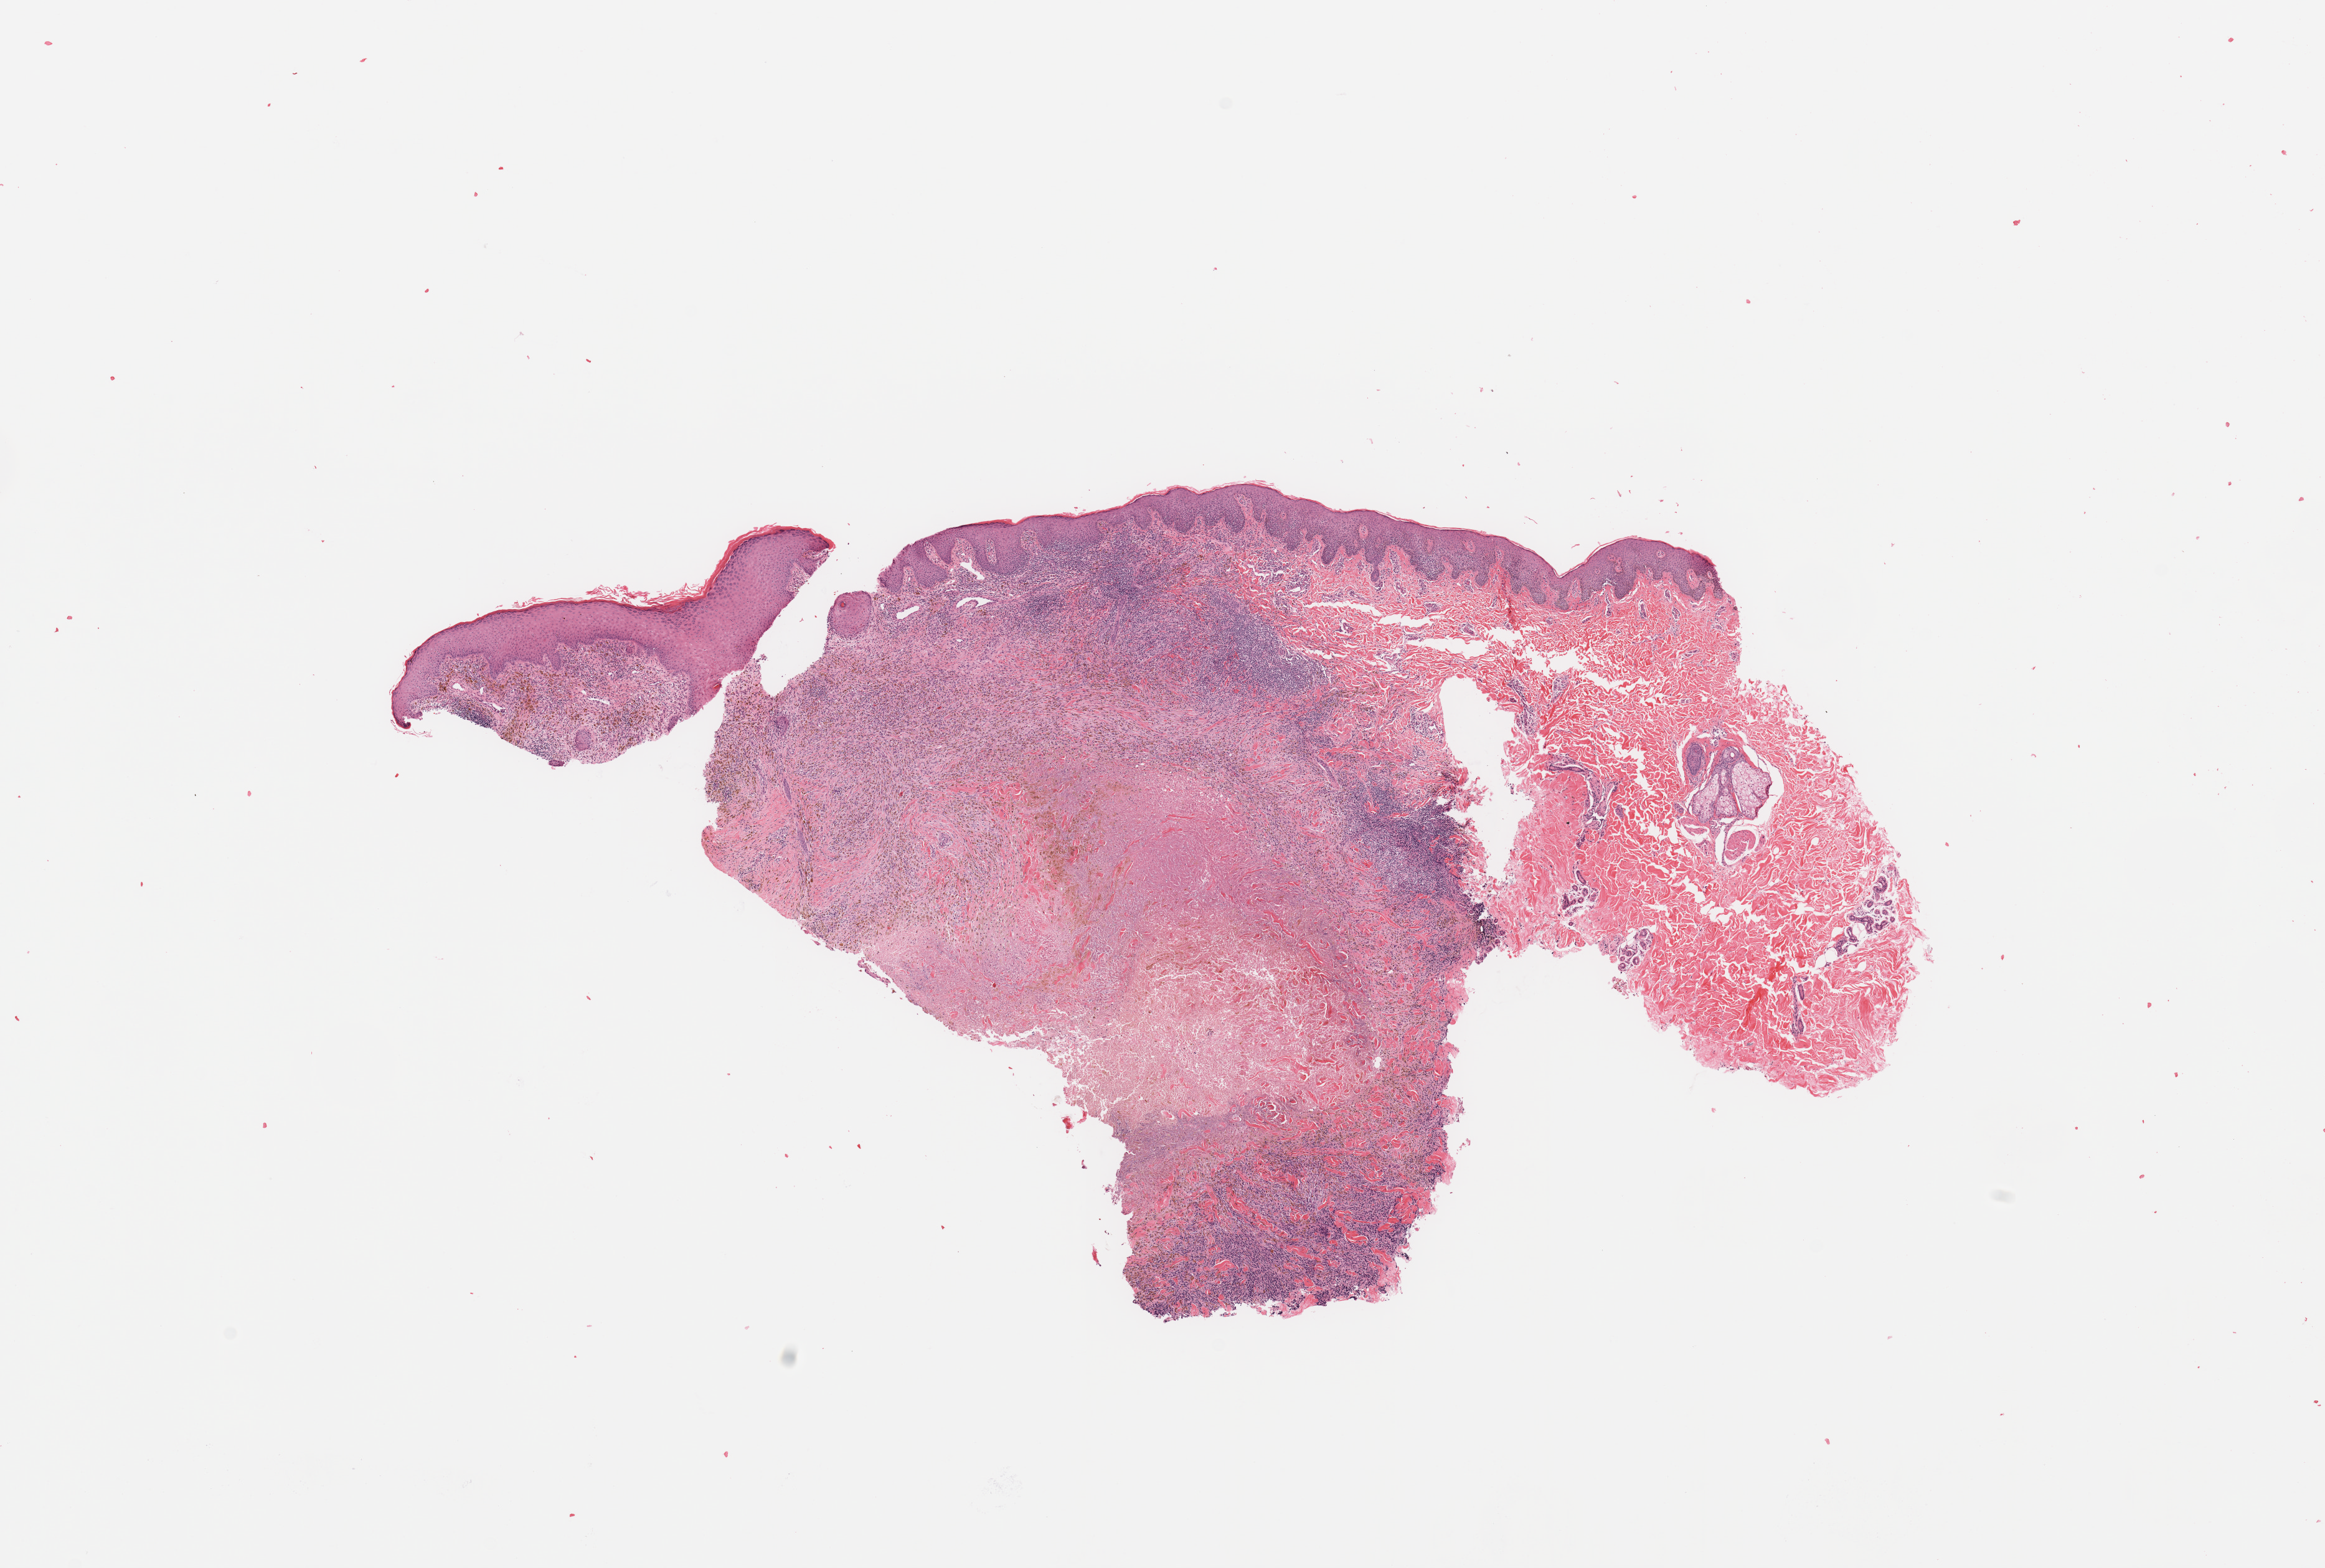
Whole-slide histology image, Hematoxylin and eosin (H&E) stained — low-resolution overview of the scanned area, about 14.8 x 10.0 mm, melanoma tumour tissue; sampled site not recorded. 45-year-old female patient.
Patient diagnosis (cohort enrolment): cutaneous melanoma (skin).